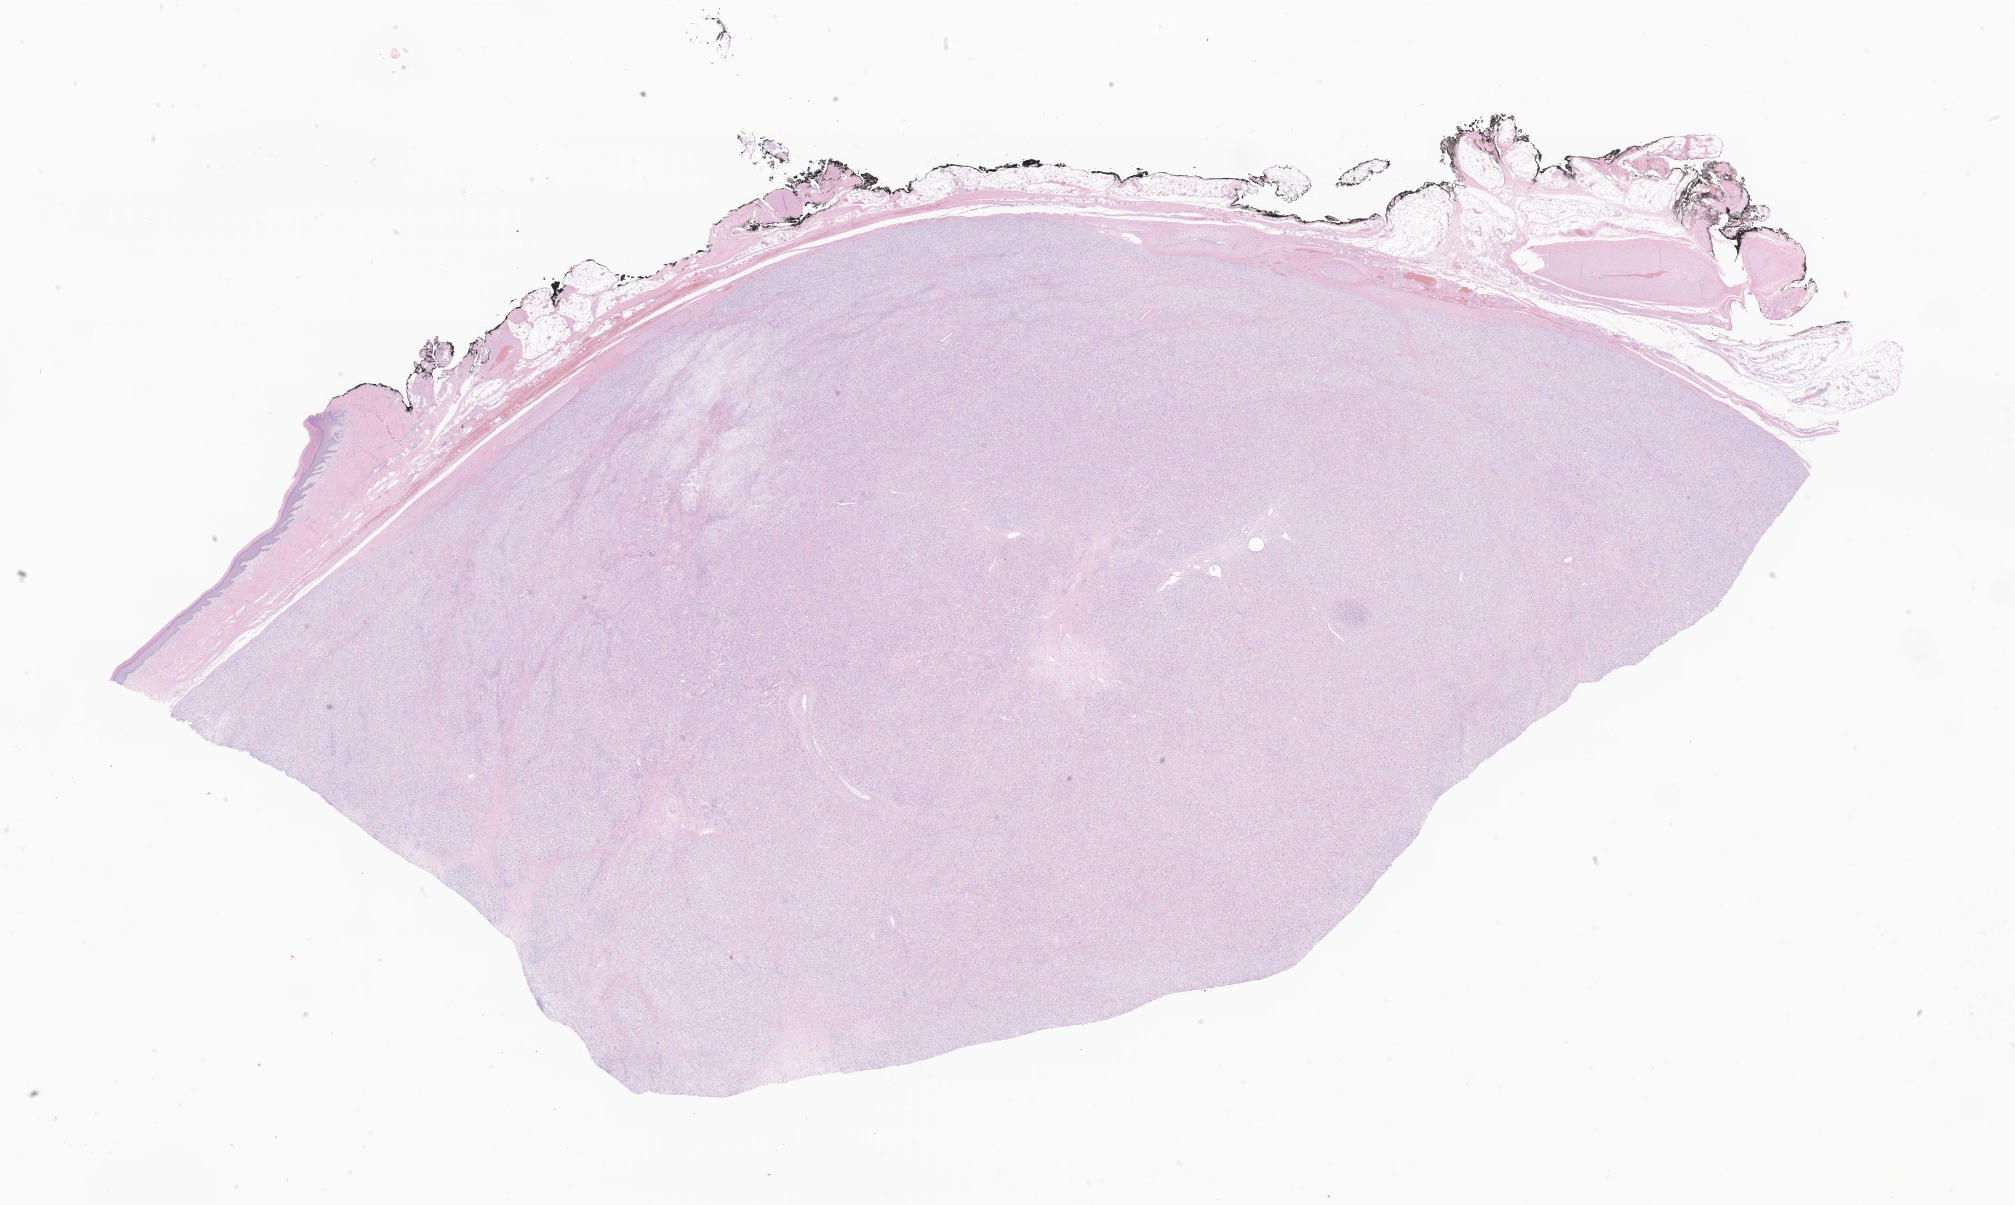
Digitized hematoxylin and eosin (H&E)-stained section of tumor tissue from the soft tissue of upper extremity — whole scanned area (about 34.0 x 20.3 mm) shown as a low-resolution overview, FFPE section. Patient female; age 204 months (17 years).
Recorded diagnosis: Neoplasm, malignant.